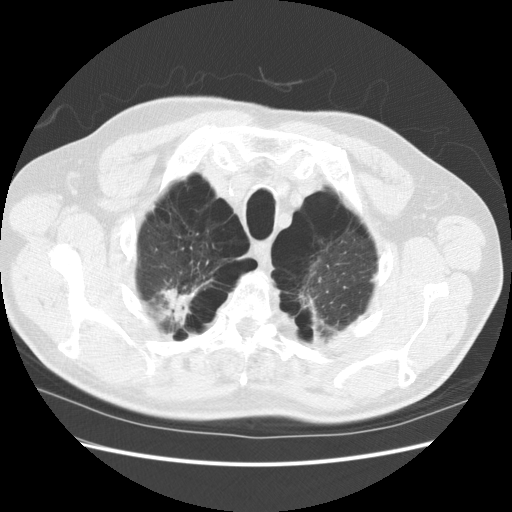
Low-dose screening chest CT, axial slice, baseline annual screen, lung window (W 1500 / L -600 HU). Male, age 68 years at enrolment.
- Expert-annotated lung lesion, box from (x=125, y=270) to (x=218, y=336) px.
- The screening reader recorded 2 non-calcified nodules or masses ≥4 mm on this exam (left lower lobe, lingula); which of them this box marks is not recorded.